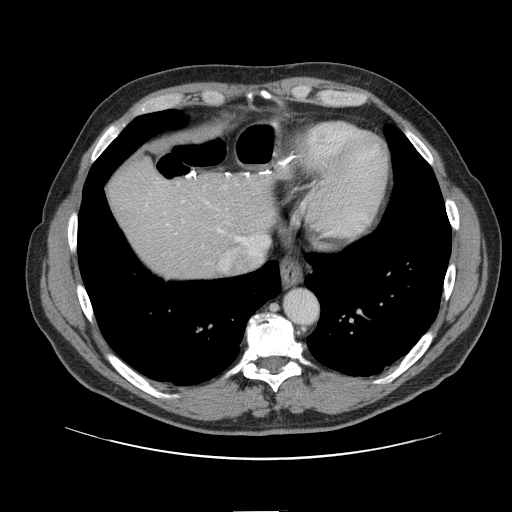
Contrast-enhanced abdominal CT, one axial slice. Slice 130 of 161 in the series (ordered by position). Soft-tissue window (W 400 / L 40 HU). 2.5 mm slice thickness. 512 × 512 image matrix. Male patient, age 66 years. Case-level facts recorded for this patient, not image findings: diagnosis: colorectal cancer liver metastases, imaged before liver resection; multiple liver metastases: no; largest metastasis: 3.5 cm.
Outlined on this slice (expert manual segmentation):
- hepatic veins: box from (x=168, y=189) to (x=267, y=271) px
- liver: (x=109, y=159)–(x=274, y=279)
- planned liver remnant (the part of the liver to remain after resection): (x=109, y=160)–(x=274, y=279)